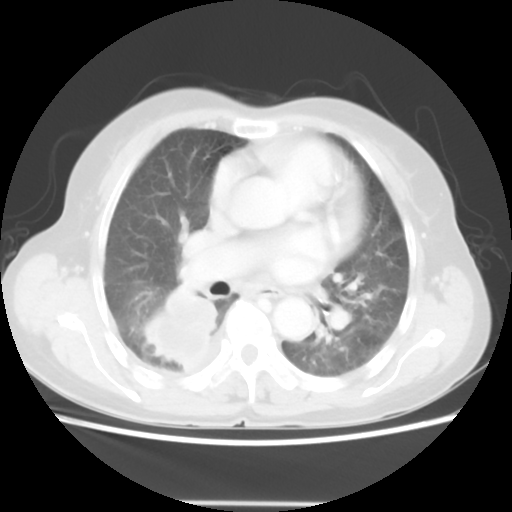
Chest CT, one axial slice; position 28 of 52 along the scan axis; reconstruction kernel STANDARD; lung window (W 1500 / L -600 HU); 5 mm slice thickness; 512 × 512 image matrix, field of view 337 × 337 mm. Patient: female, 67 years. From the clinical record (not read from this slice): clinical TNM (as recorded): T3 N1 M1.
Annotated regions visible in this slice (bounding box drawn by a radiologist):
- lung tumour (recorded histology: adenocarcinoma): bounding box (x1, y1, x2, y2) in pixels: (137, 285, 223, 379)